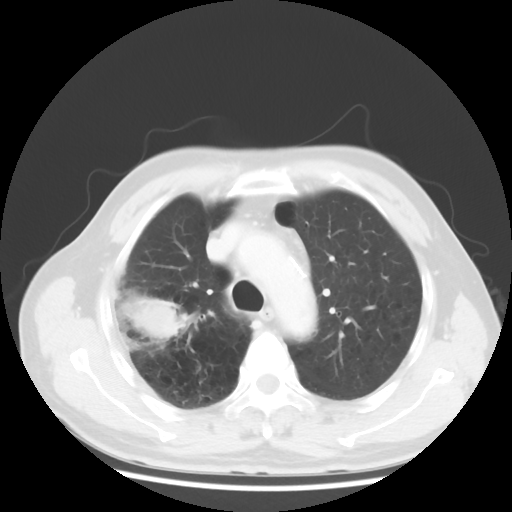
Chest CT, one axial slice; position 37 of 50 along the scan axis; reconstruction kernel STANDARD; 120 kVp; lung window (W 1500 / L -600 HU); 5 mm slice thickness; 512 × 512 image matrix, field of view 360 × 360 mm. Male patient, age 69 years. Case-level facts recorded for this patient, not image findings: clinical TNM (as recorded): T3 N0 M0; histopathological grade: G3.
Structures marked on this image (rectangle marked by the reading radiologist):
- lung tumour (recorded histology: adenocarcinoma): bounding box [x1, y1, x2, y2] px = [111, 279, 201, 356]